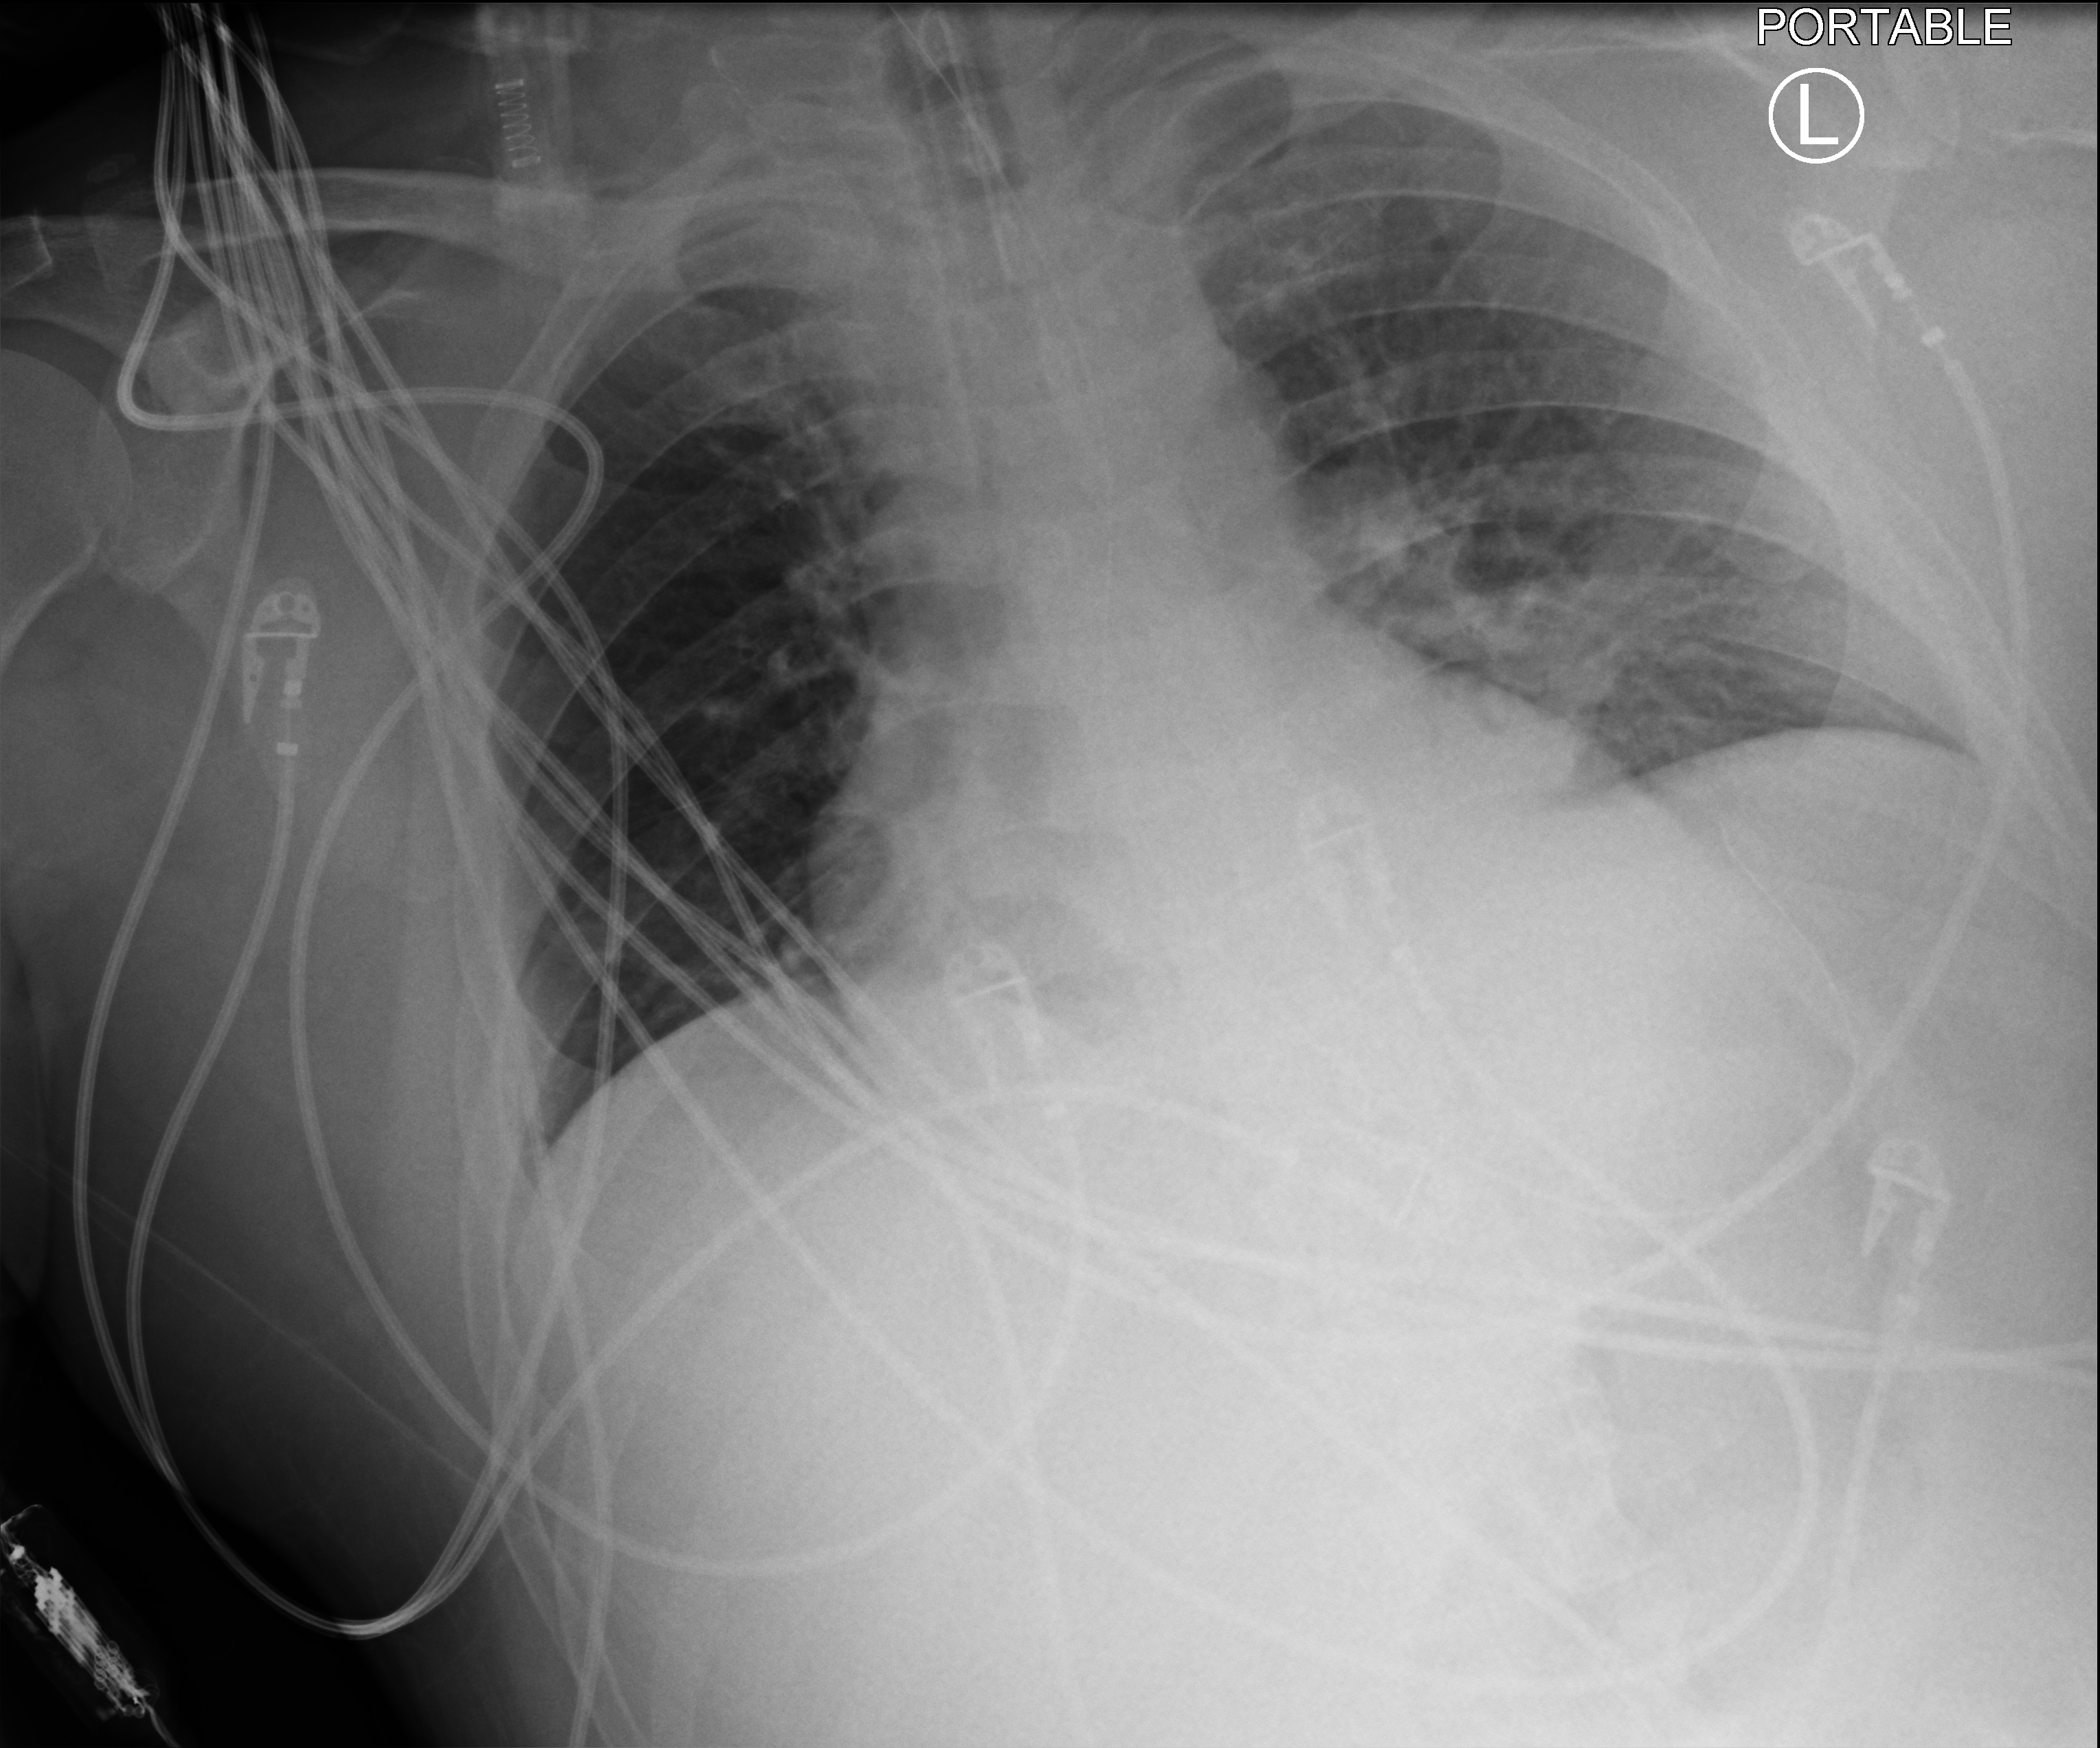
Portable chest radiograph. Patient hospitalised with COVID-19; male, aged 18–59 years.
Hospital-stay facts (about this admission, not read from this image; timing relative to this image not recorded): length of hospital stay: 65 days; mechanically ventilated during this hospital stay: yes; admitted to intensive care during this hospital stay: yes.